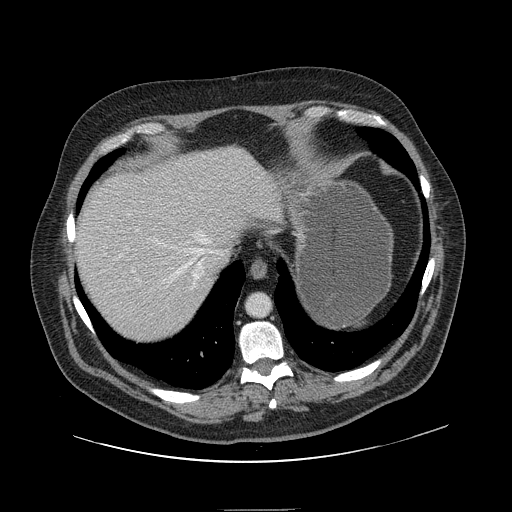
Contrast-enhanced abdominal CT, one axial slice. Position 124 of 154 along the scan axis. 120 kVp. Intravenous contrast given. Soft-tissue window (W 400 / L 40 HU). 2.5 mm slice thickness. 512 × 512 image matrix, field of view 451 × 451 mm. Male patient, age 61 years. Case-level facts recorded for this patient, not image findings: diagnosis: colorectal cancer liver metastases, imaged before liver resection; multiple liver metastases: yes; largest metastasis: 2.6 cm; disease in both lobes: yes.
Annotated regions visible in this slice (manually delineated by an expert):
- hepatic veins: bounding box [x1, y1, x2, y2] px = [116, 233, 213, 290]
- liver: [76, 148, 277, 344]
- planned liver remnant (the part of the liver to remain after resection): [76, 148, 275, 344]
- portal vein (with intrahepatic branches): [128, 214, 140, 282]